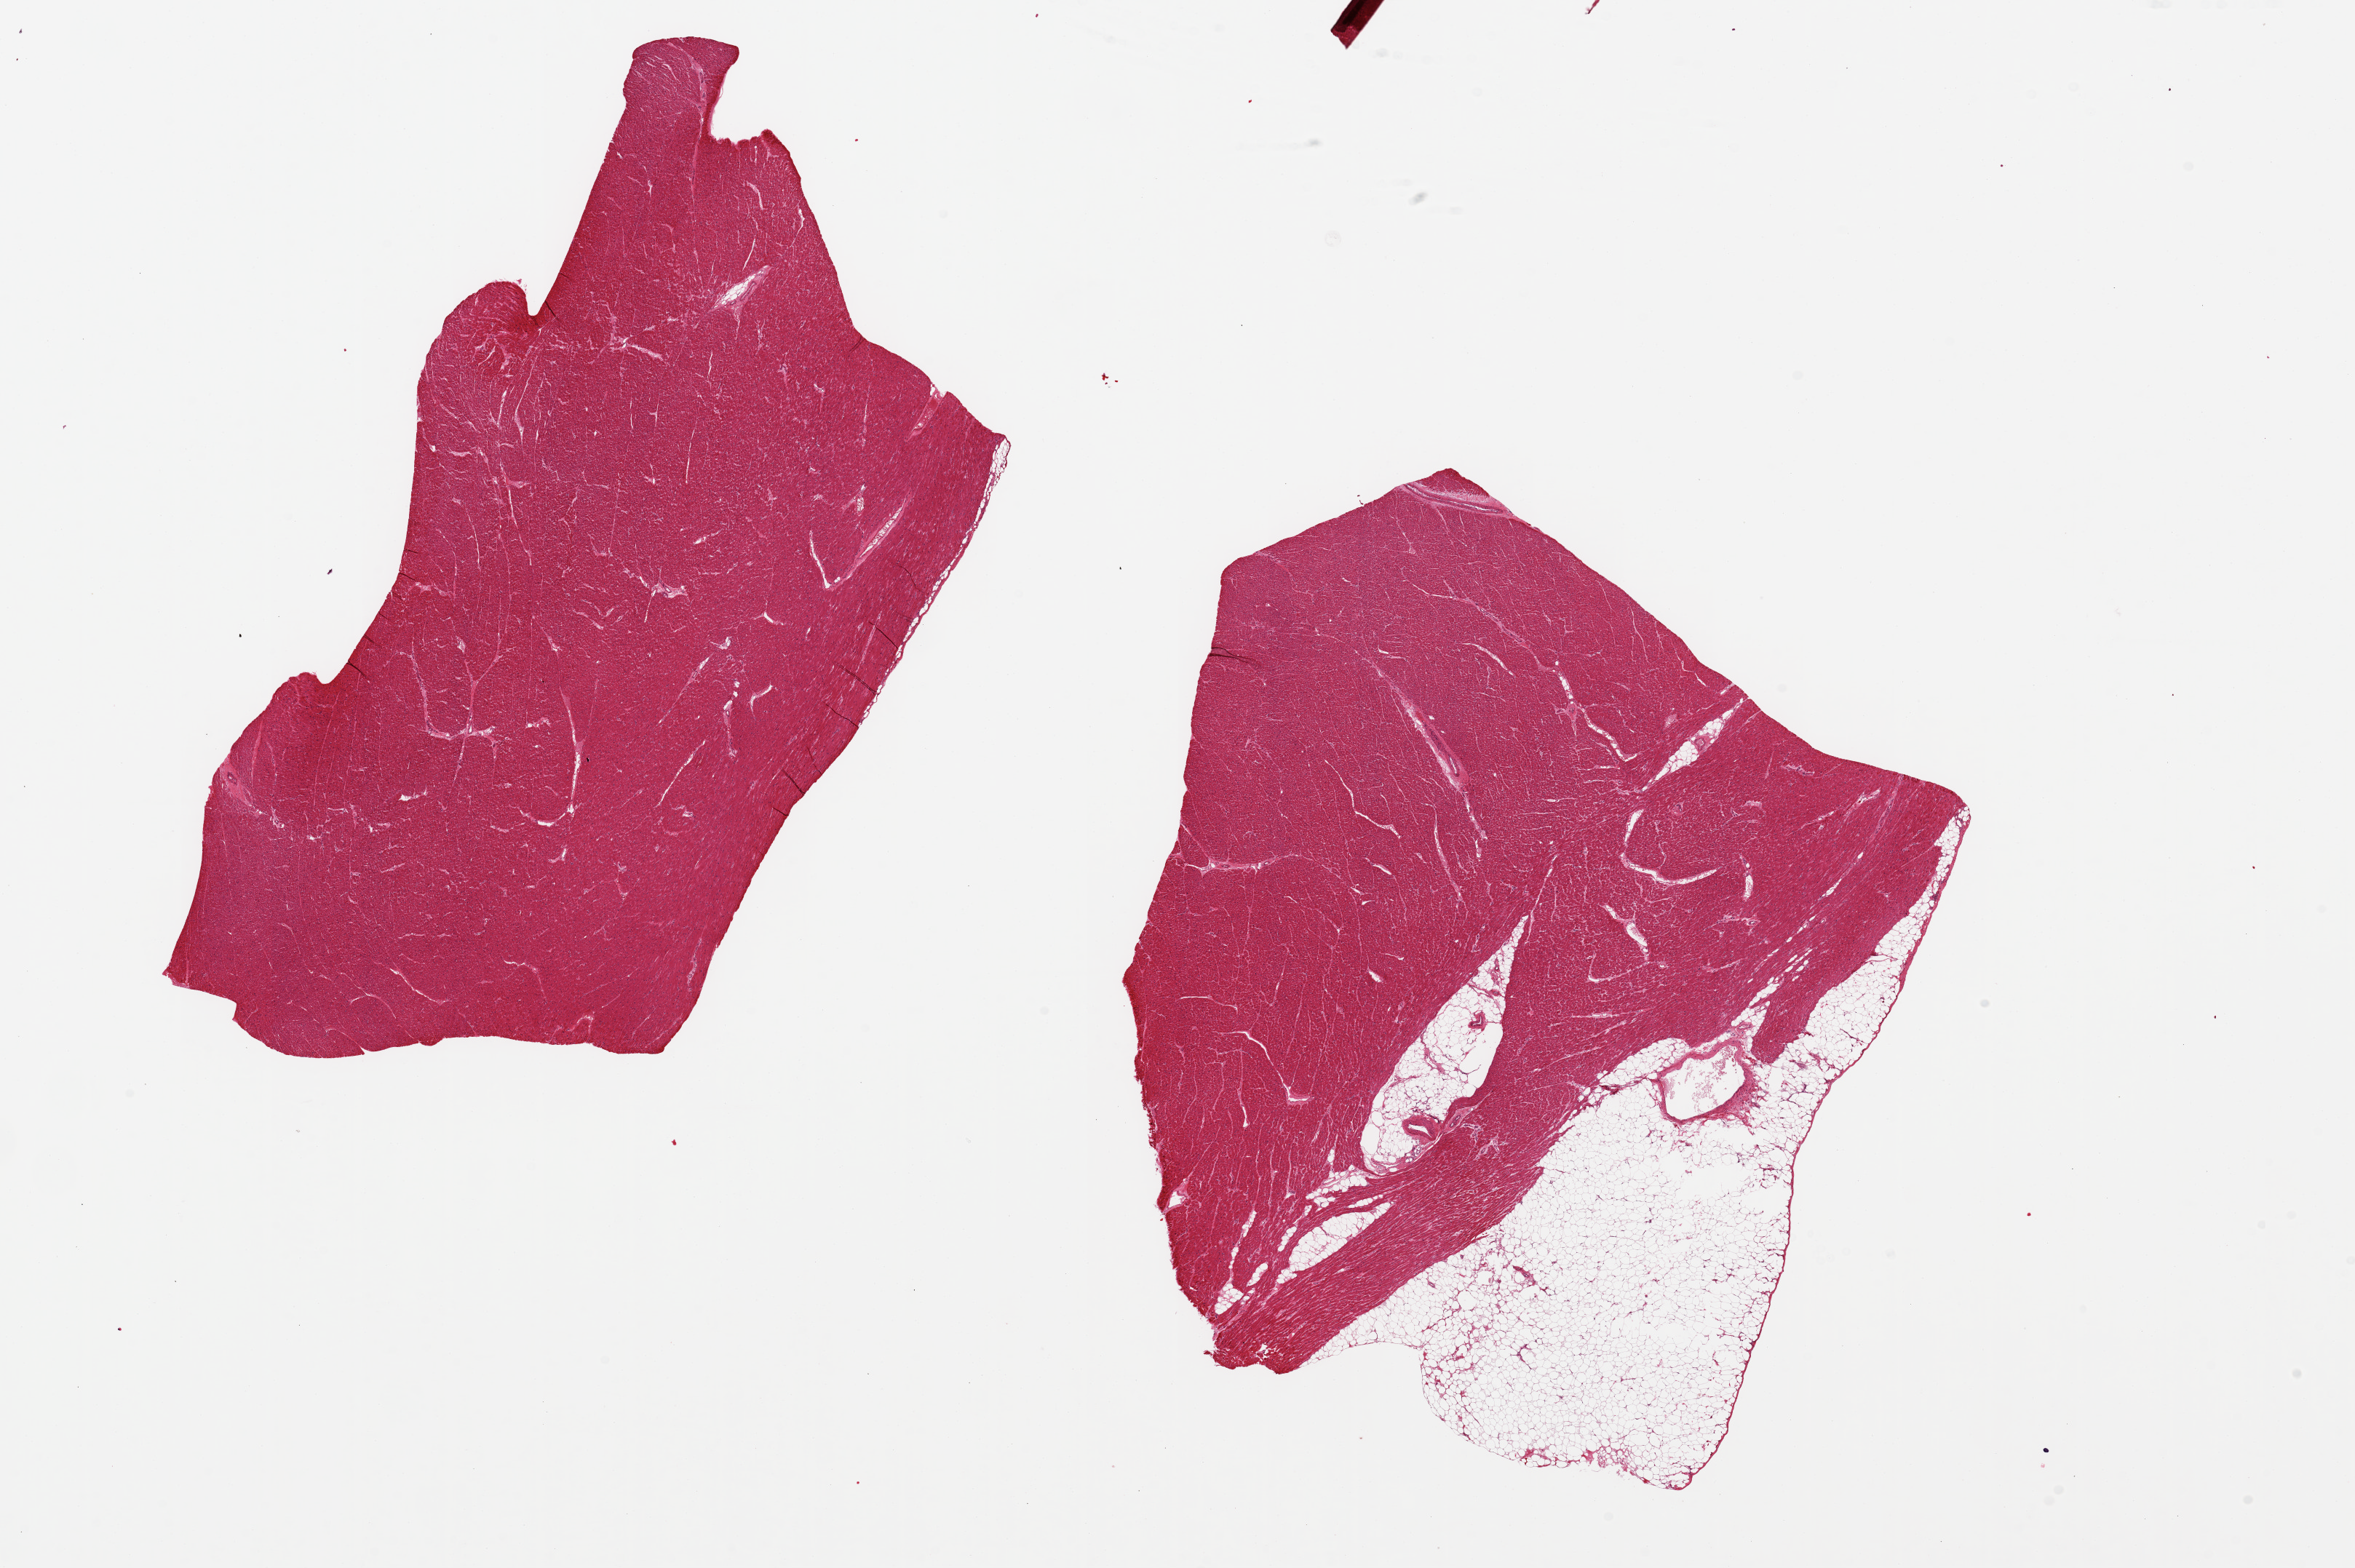
Whole-slide image, haematoxylin and eosin stain — a low-resolution overview of the entire scanned area, about 25.6 x 17.0 mm, PAXgene-fixed, paraffin-embedded tissue, sampled site (target tissue): heart, tissue donor sample. Donor: male.
* review note (as recorded): 2 pieces ~10x8mm. Minimal ischemic damage